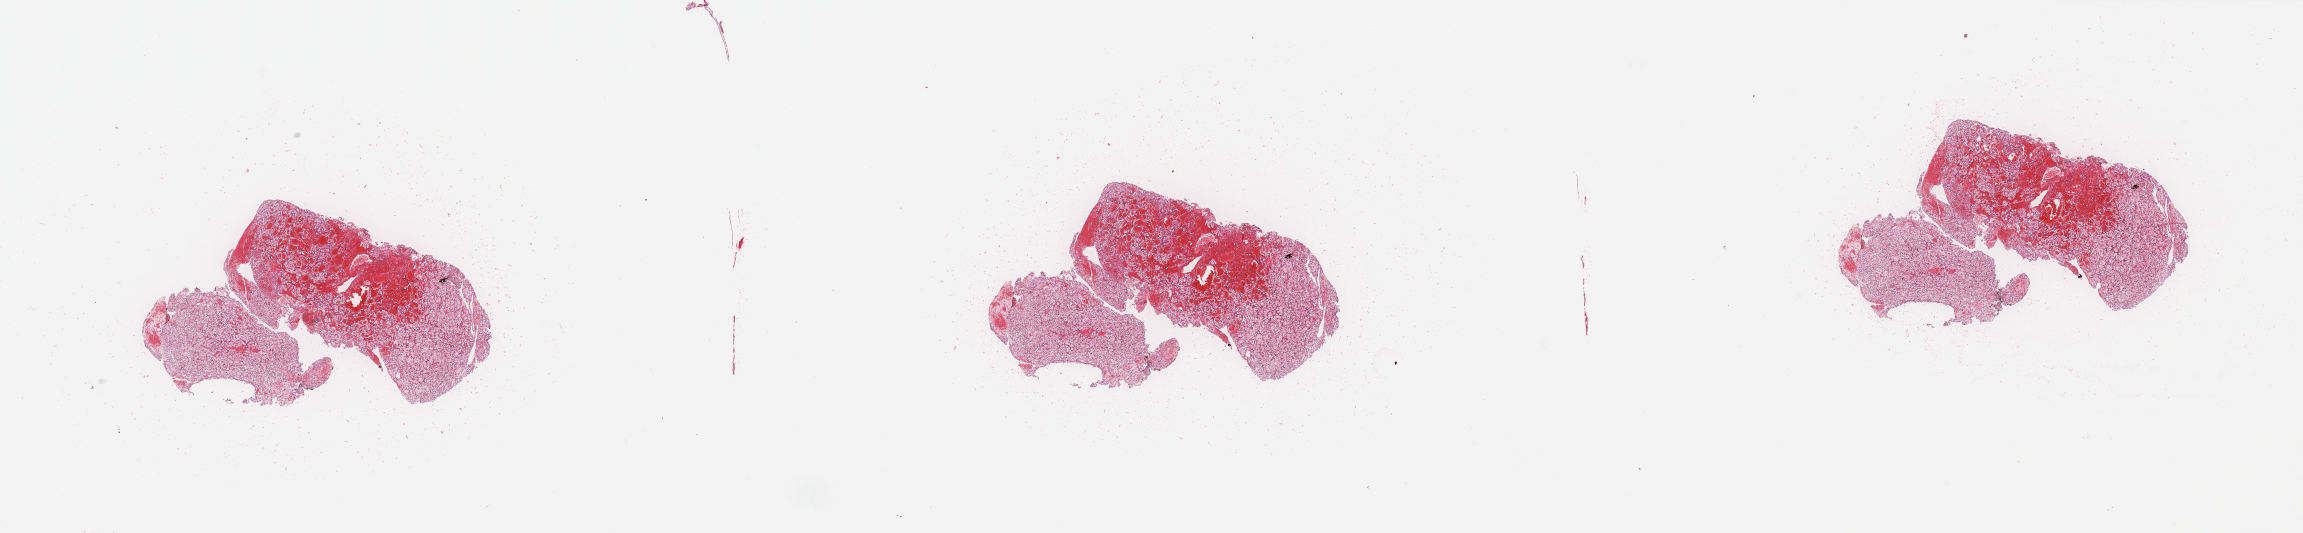
Digitized Hematoxylin and eosin (H&E) stained tissue section (whole slide), low-resolution overview of the scanned area, about 36.4 x 8.4 mm; kidney, tumour tissue. 62-year-old male patient. Histologic grade: G3 (poorly differentiated).
Histologic diagnosis: Renal cell carcinoma, NOS. Primary tumour site (as recorded): lower pole.